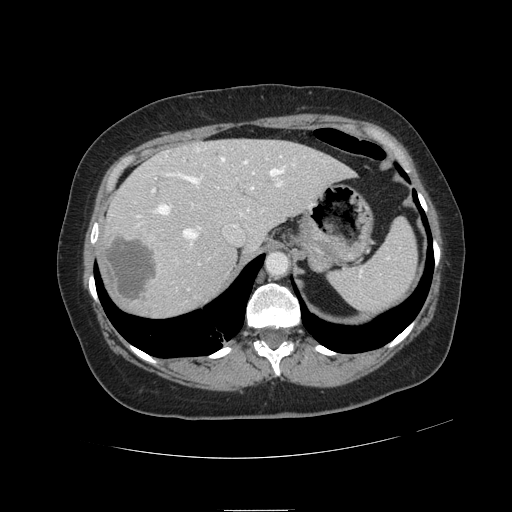
Contrast-enhanced abdominal CT, one axial slice. Slice 86 of 121 in the series (ordered by position). Soft-tissue window (W 400 / L 40 HU). 2.5 mm slice thickness. 512 × 512 image matrix, field of view 400 × 400 mm. Female patient, age 52 years. Case-level facts recorded for this patient, not image findings: diagnosis: colorectal cancer liver metastases, imaged before liver resection; multiple liver metastases: yes; largest metastasis: 6.3 cm; disease in both lobes: no.
Annotated regions visible in this slice (outlined manually by an expert reader):
- hepatic veins: bounding box (x1, y1, x2, y2) in pixels: (136, 149, 294, 239)
- liver: (103, 140, 350, 315)
- planned liver remnant (the part of the liver to remain after resection): (168, 140, 351, 247)
- portal vein (with intrahepatic branches): (152, 158, 283, 290)
- liver metastasis: (105, 235, 157, 303)